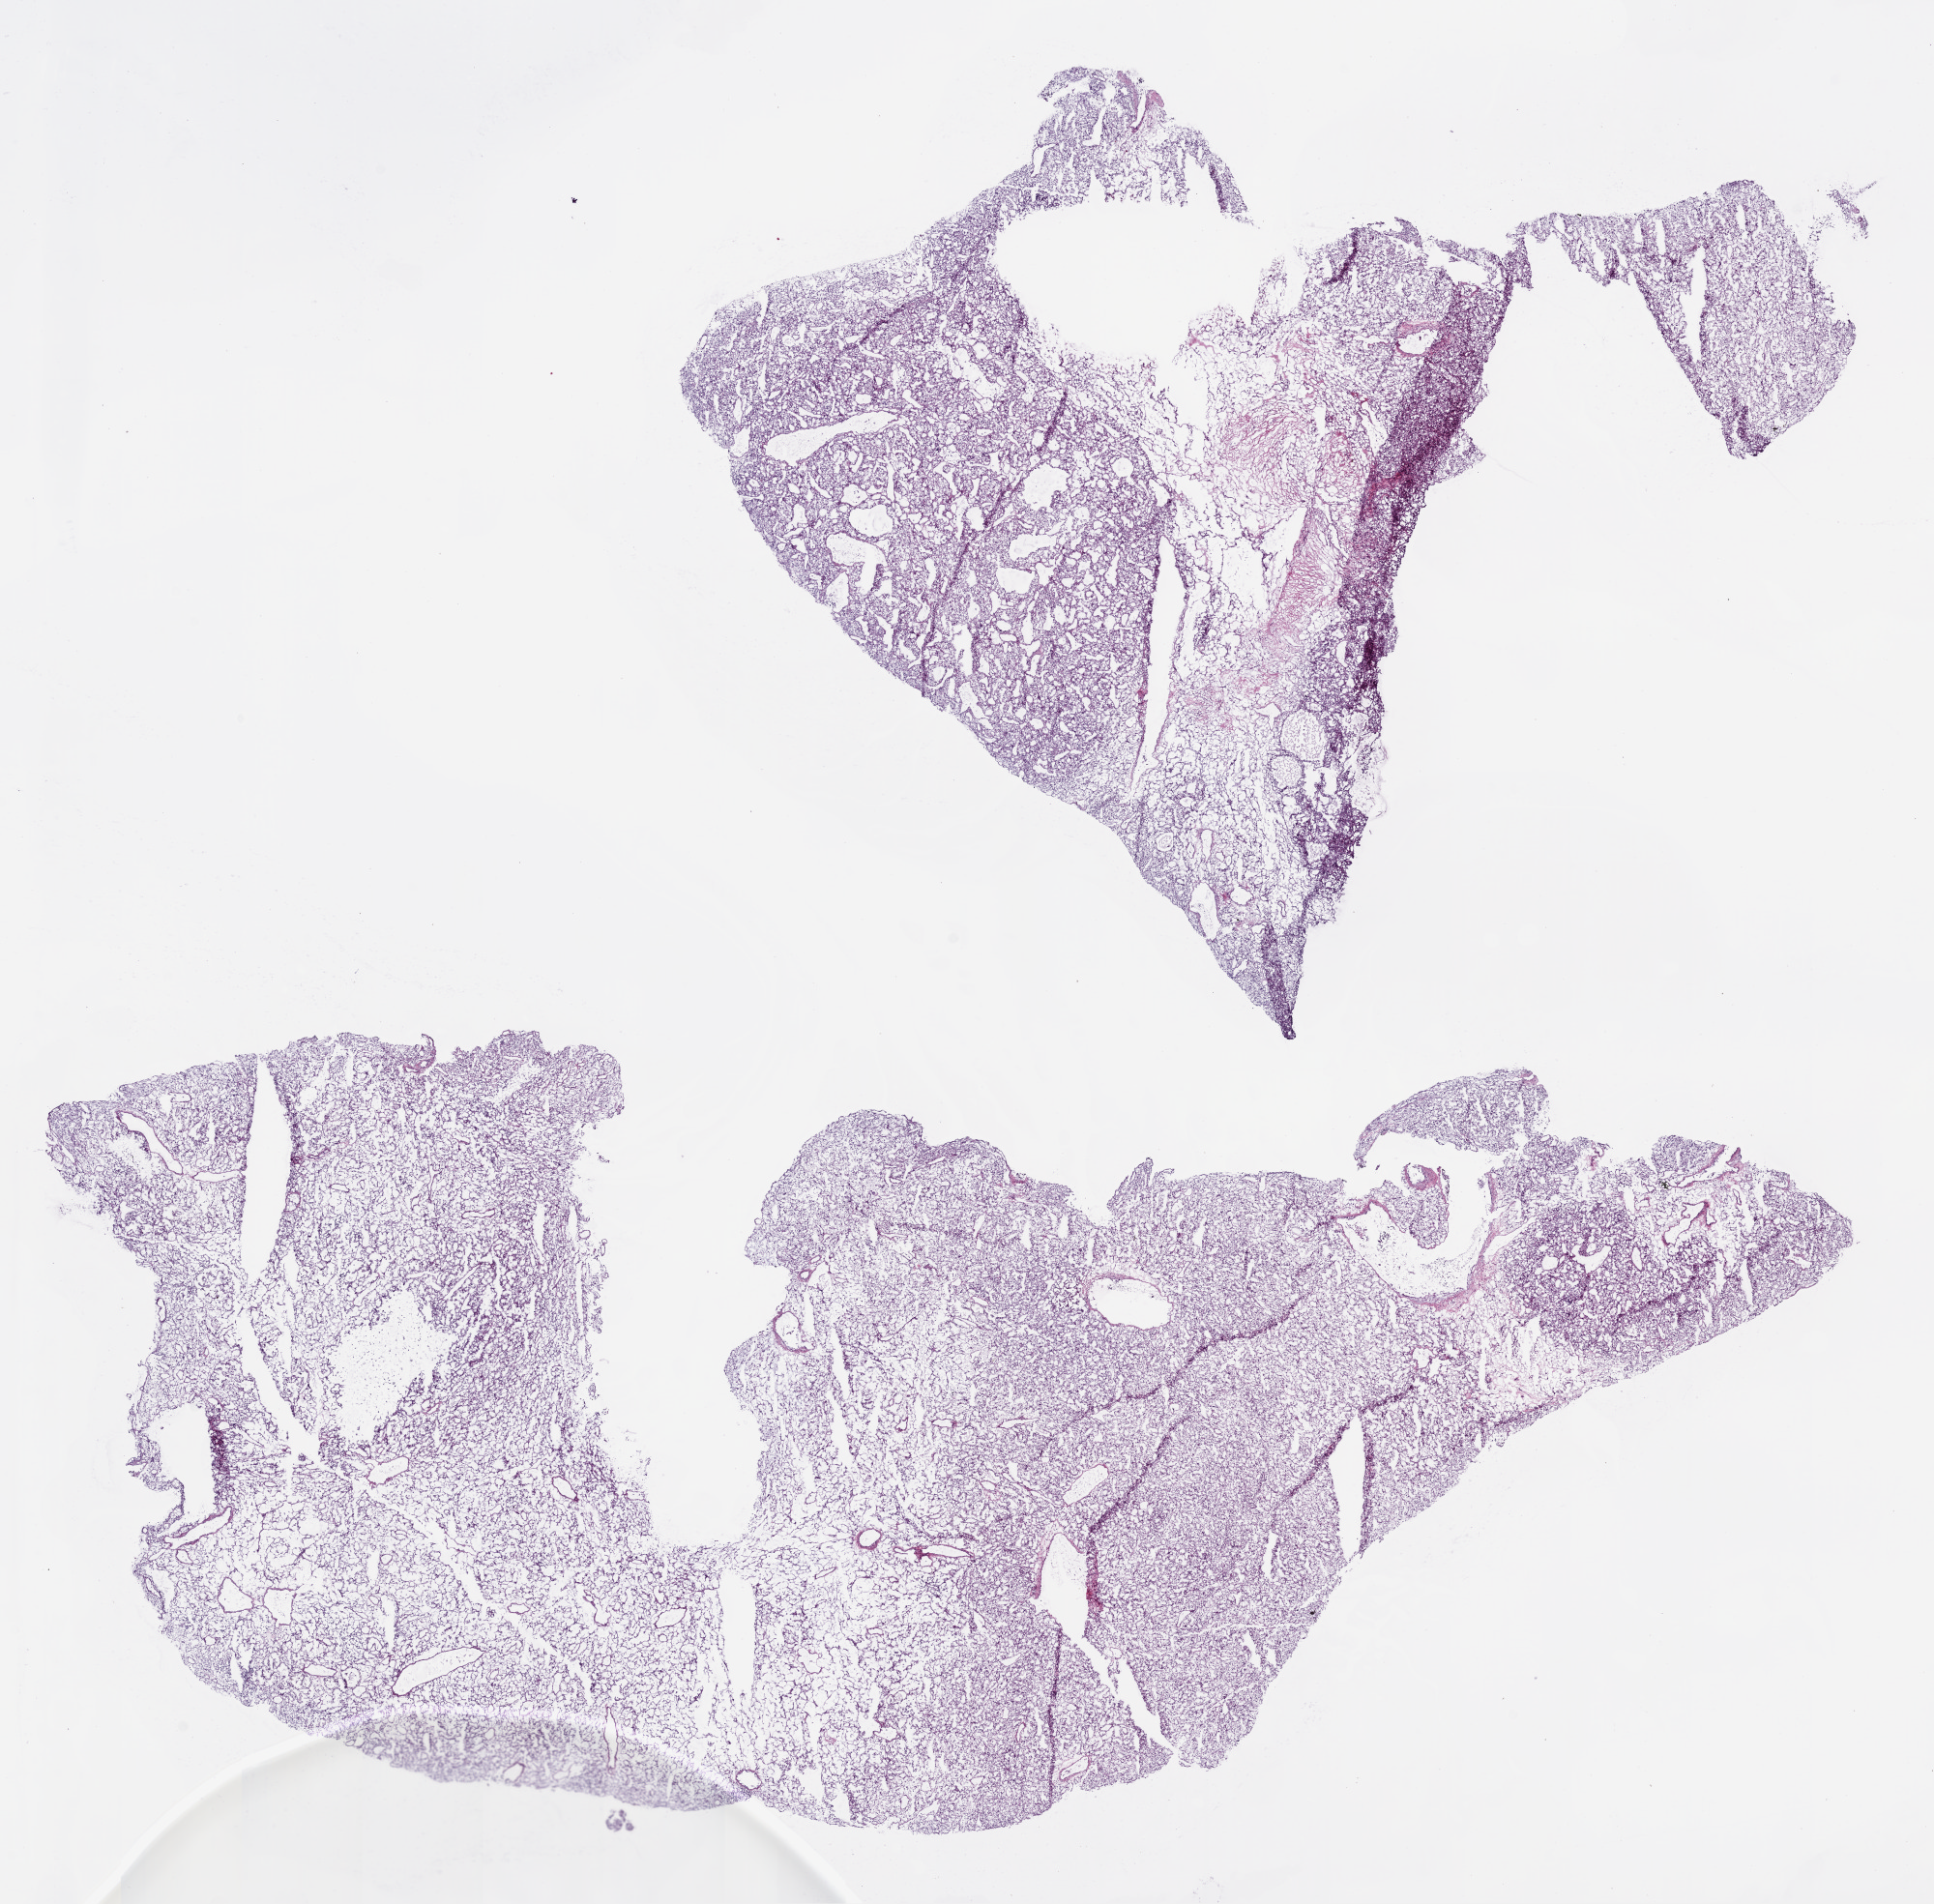
H&E whole-slide image — a low-resolution overview of the entire scanned area, about 16.0 x 15.8 mm (slide scanned at 20x), frozen section, sample: primary tumour, kidney. Male, age 75 years at initial diagnosis. Histologic grade: G2 (moderately differentiated). Slide review estimates, as recorded: tumour cells 90%, tumour nuclei 90%, normal cells 0%, stromal cells 10%, necrosis 0%.
• histologic diagnosis: Clear cell adenocarcinoma, NOS
• AJCC pathologic stage: I